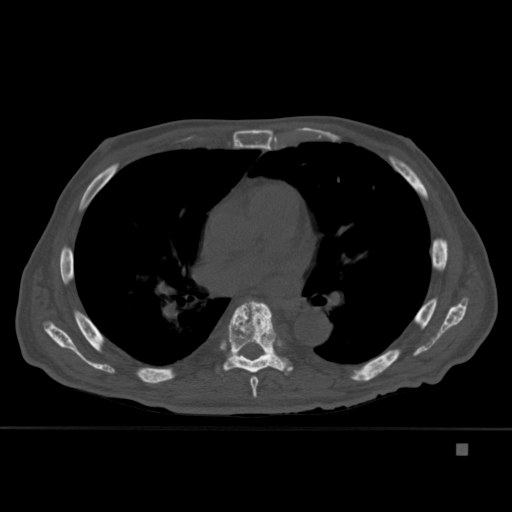
CT including the spine, one axial slice; position 281 of 451 along the scan axis; bone window (W 1800 / L 400 HU); 512 × 512 image matrix, field of view 378 × 378 mm. Patient: male, 75 years. Case-level facts recorded for this patient, not image findings: primary cancer: prostate.
Outlined on this slice (semi-automatically segmented with operator editing):
- T4 vertebra: bounding box <270,321,277,336> (left, top, right, bottom; pixels)
- T6 vertebra: <250,376,259,398>
- T7 vertebra: <217,300,293,375>
- T8 vertebra: <236,354,241,356>